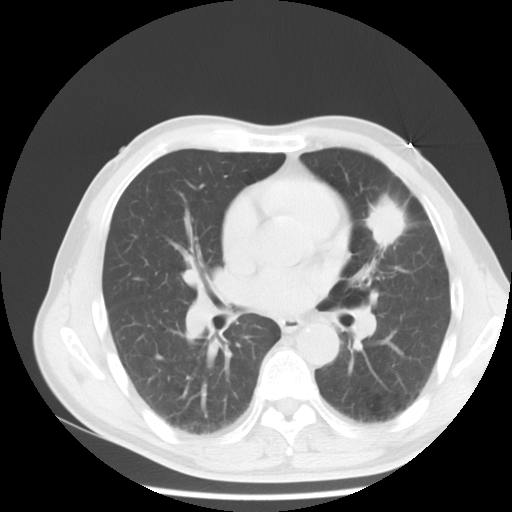
Chest CT, one axial slice. Slice 7 of 13 in the series (ordered by position). Reconstruction kernel STANDARD. Lung window (W 1500 / L -600 HU). 512 × 512 image matrix. Patient: male, 54 years. From the clinical record (not read from this slice): clinical TNM (as recorded): T1c N0 M0.
Structures marked on this image (bounding box drawn by a radiologist):
- lung tumour (recorded histology: adenocarcinoma): bounding box <367,197,407,245> (left, top, right, bottom; pixels)